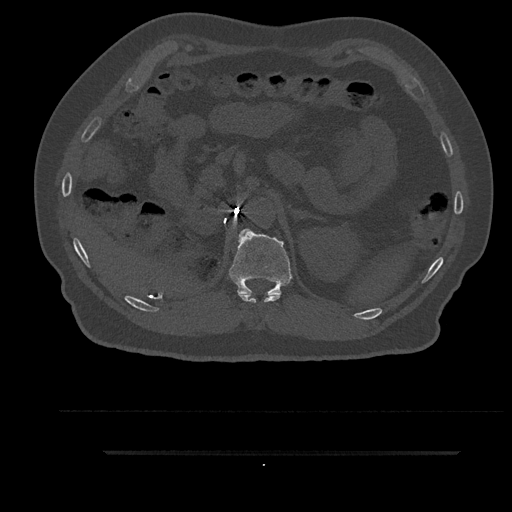
CT including the spine, one axial slice; position 265 of 797 along the scan axis; 120 kVp; bone window (W 1800 / L 400 HU); 512 × 512 image matrix. Male patient, age 63 years. From the clinical record (not read from this slice): primary cancer: renal.
Outlined on this slice (semi-automatic segmentation, software-assisted and operator-edited):
- T11 vertebra: bounding box (x1, y1, x2, y2) in pixels: (238, 293, 281, 303)
- T12 vertebra: (229, 228, 292, 297)